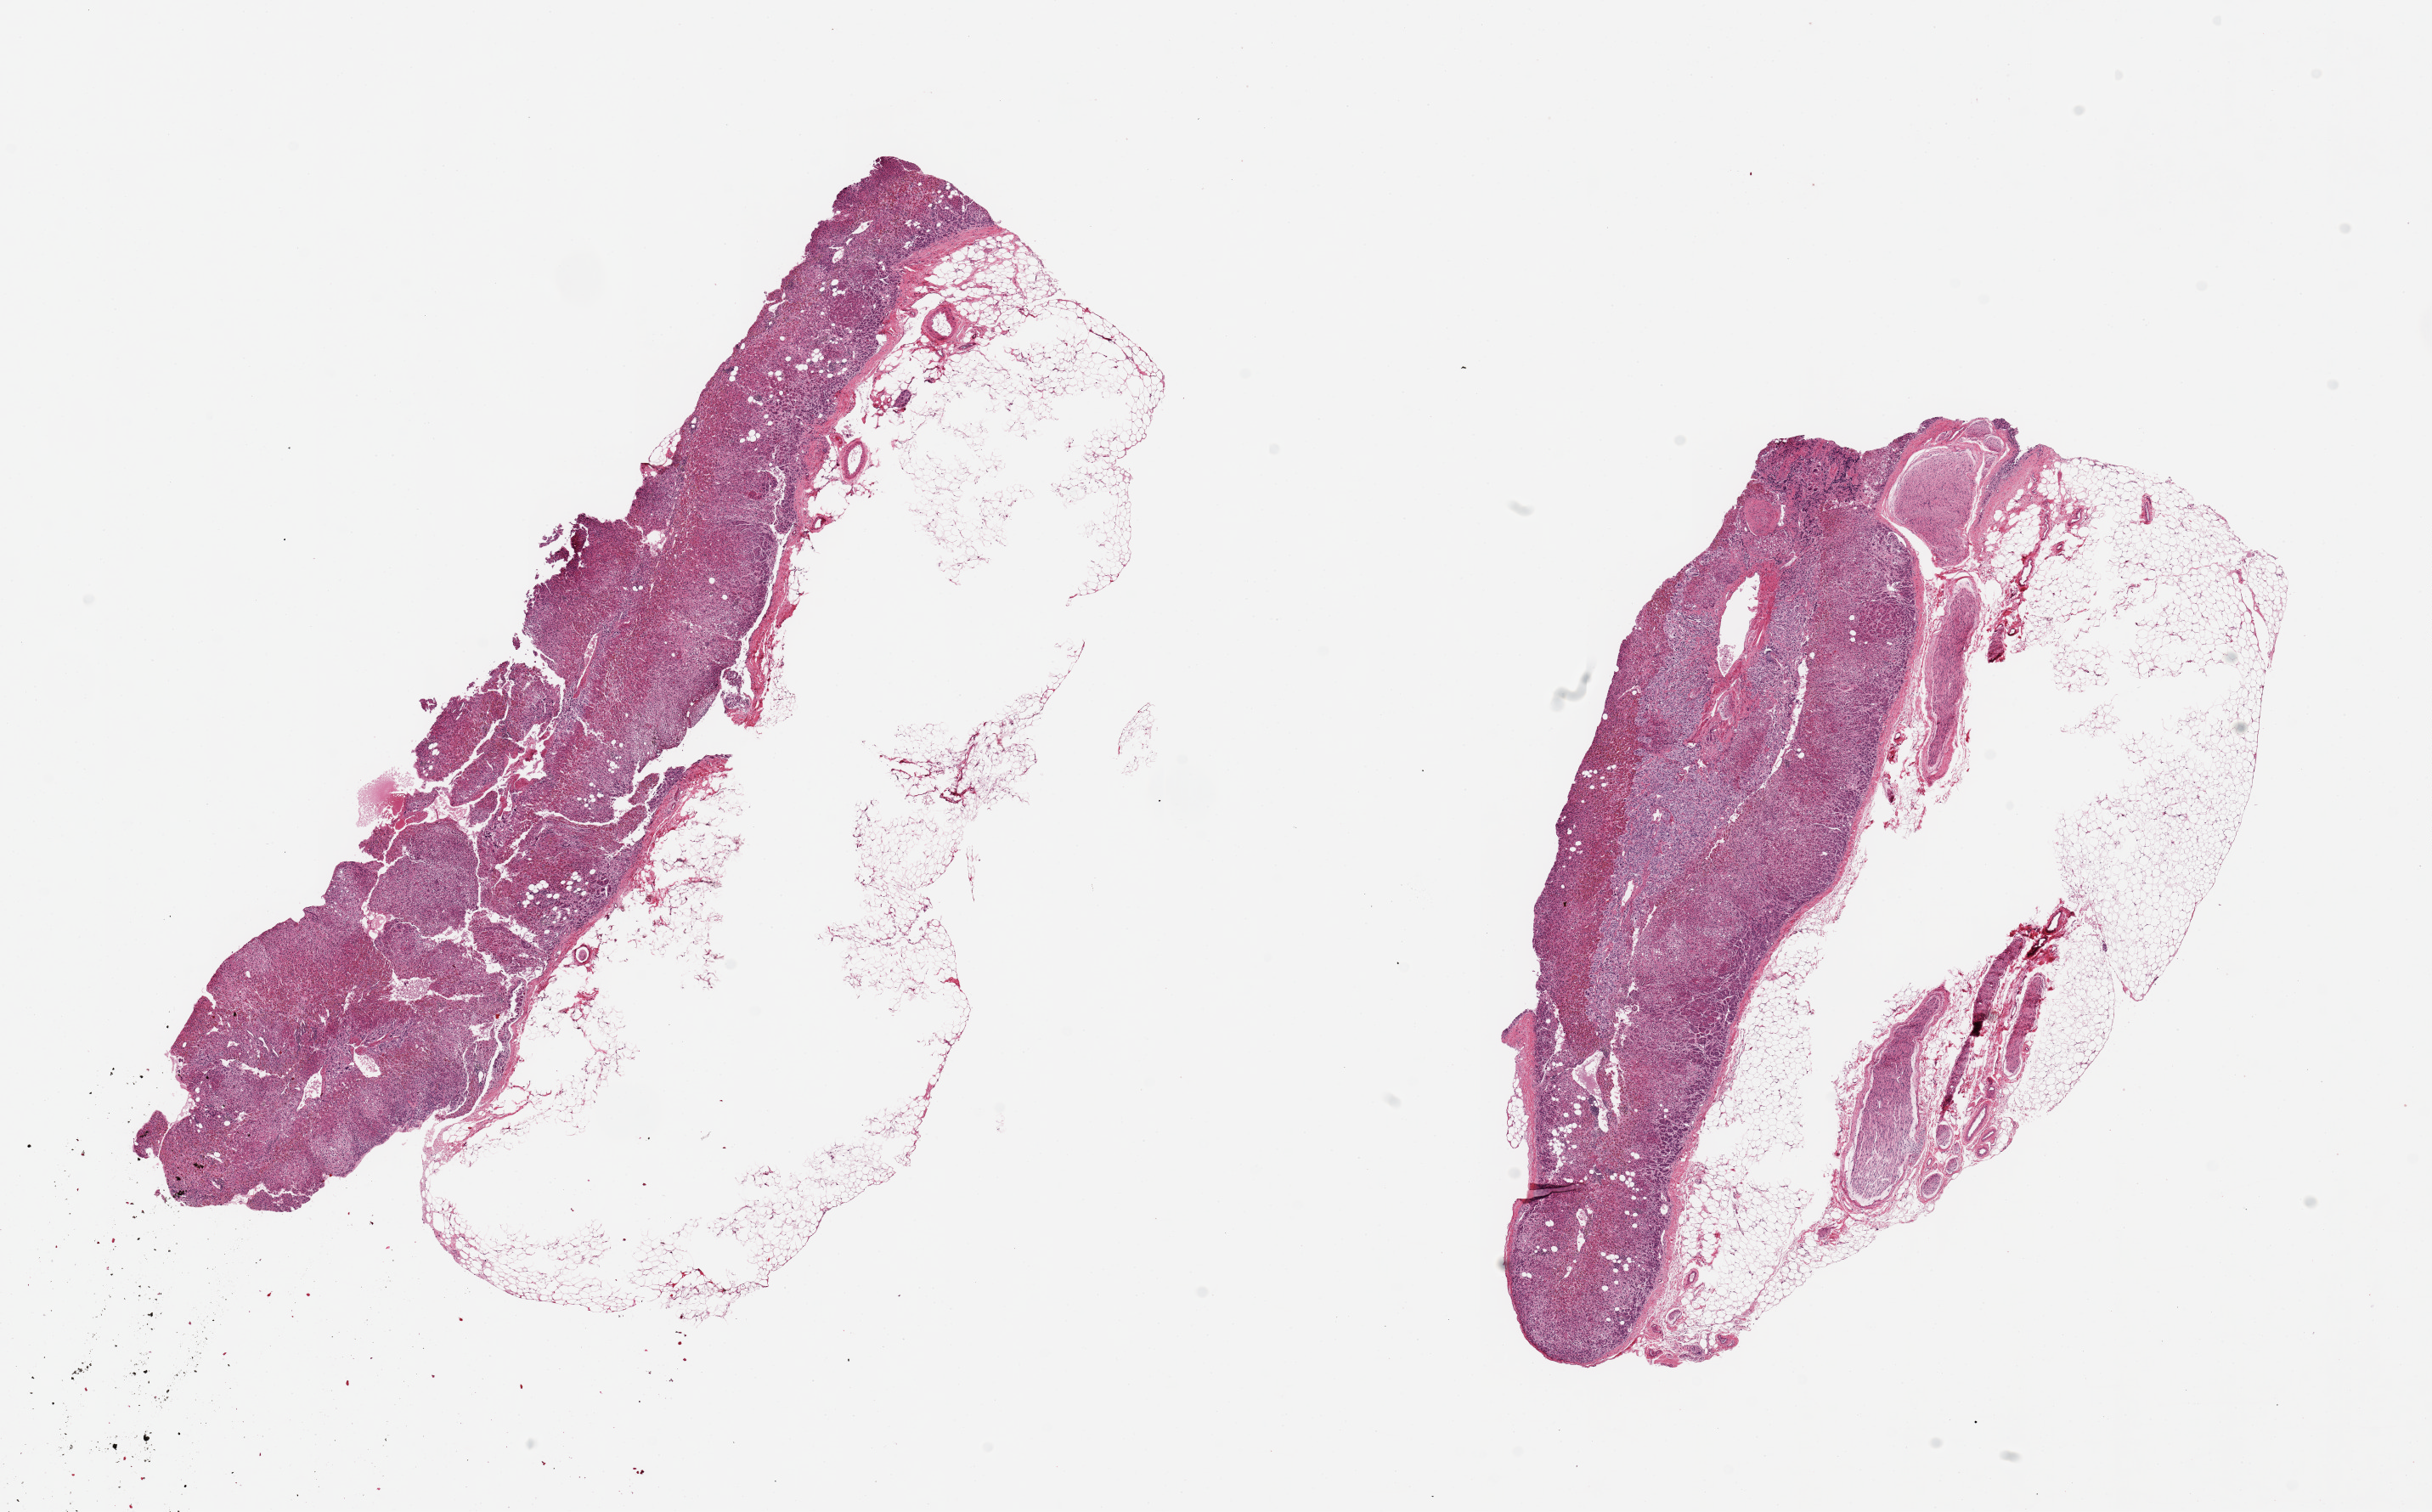
Whole-slide image, haematoxylin and eosin stain — shown as a low-resolution overview of the whole scanned area (about 22.6 x 14.1 mm). PAXgene-fixed, paraffin-embedded tissue. Section of adrenal gland (target tissue). Donor tissue sample. Donor sex: male.
• reviewer comment on this tissue sample: 2 pieces 12x6 & 9x6 mm; mostly cortex; >50% poorly fixed adipose; several large nerves in one piece, ~10%